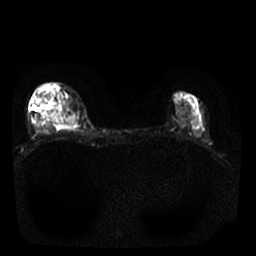
Breast MRI, one axial slice; slice 10 of 25 in the series (ordered by position); diffusion-weighted series; image 2 of 4 stored at this slice position (different b-values; order by instance number); 1.5 T; 4 mm slice thickness; 256 × 256 image matrix. Female patient.
Annotated regions visible in this slice (outlined manually by an expert reader):
- tumour on diffusion-weighted imaging: bounding box <51,114,75,126> (left, top, right, bottom; pixels)